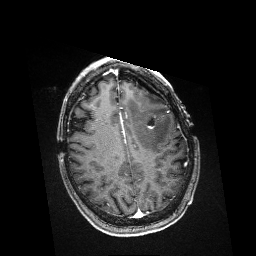
Brain MRI from a brain-tumour surgery series, one axial slice. Position 119 of 176 along the scan axis. T1-weighted post-contrast. 1 mm slice thickness. 256 × 256 image matrix, field of view 256 × 256 mm. From the clinical record (not read from this slice): histopathology: Metastatic Melanoma; tumour location: Left Frontal.
Structures marked on this image (outlined manually by an expert reader):
- residual tumour: bounding box [x1, y1, x2, y2] px = [147, 125, 154, 129]